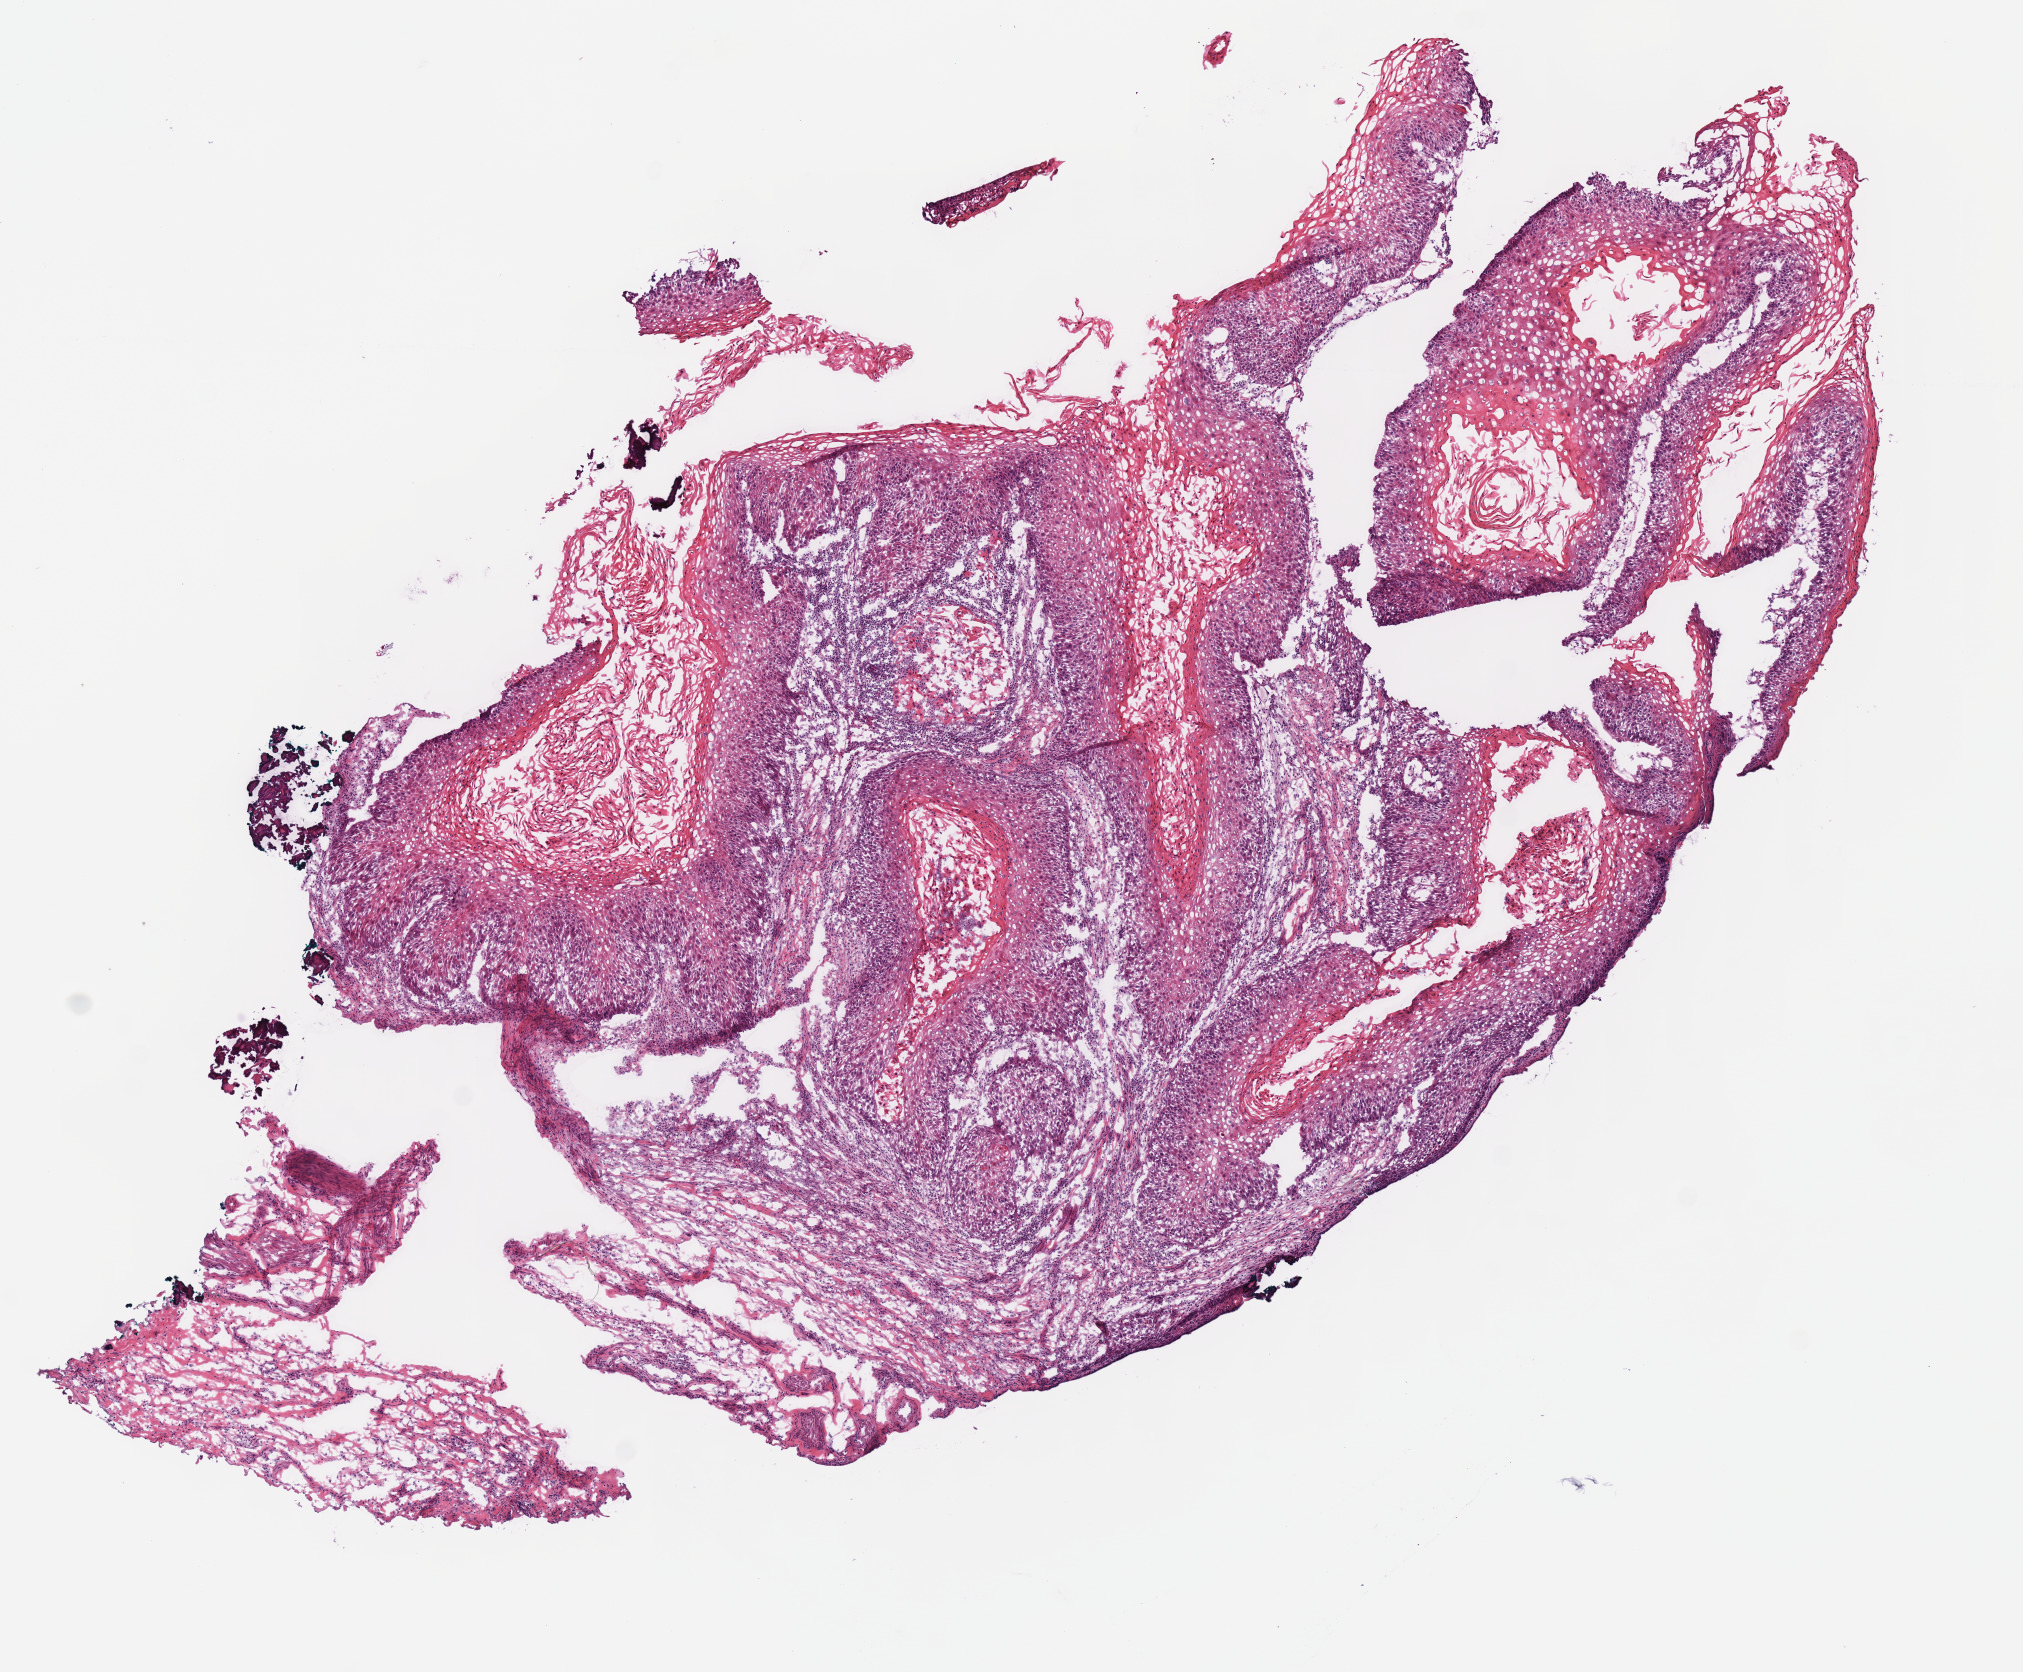
Hematoxylin and eosin (H&E) stained whole-slide image, low-resolution overview of the scanned area, about 8.0 x 6.6 mm, frozen section from the bottom of the tissue portion, sample: primary tumour, head and neck. Female, age 77 years at initial diagnosis.
Pathologic diagnosis: Squamous cell carcinoma, NOS (overlapping lesion of lip, oral cavity and pharynx).